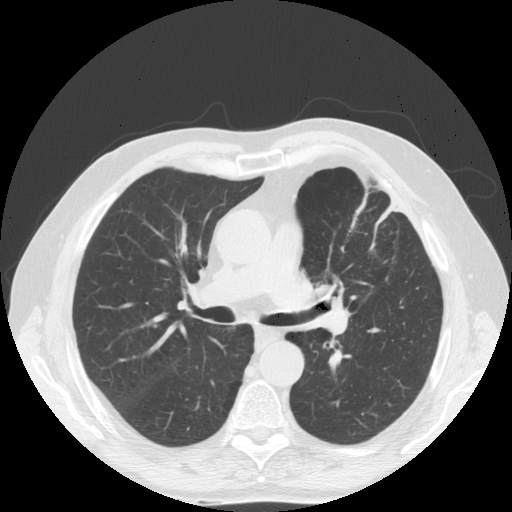
Low-dose screening chest CT, one axial slice; slice 107 of 170 in the series (ordered by position); reconstruction kernel STANDARD; 140 kVp; lung window (W 1500 / L -600 HU); 2.5 mm slice thickness; 512 × 512 image matrix.
Outlined on this slice (outlined manually by an expert reader):
- lesion 1 (tumor, upper lobe of left lung): box from (x=315, y=283) to (x=336, y=298) px